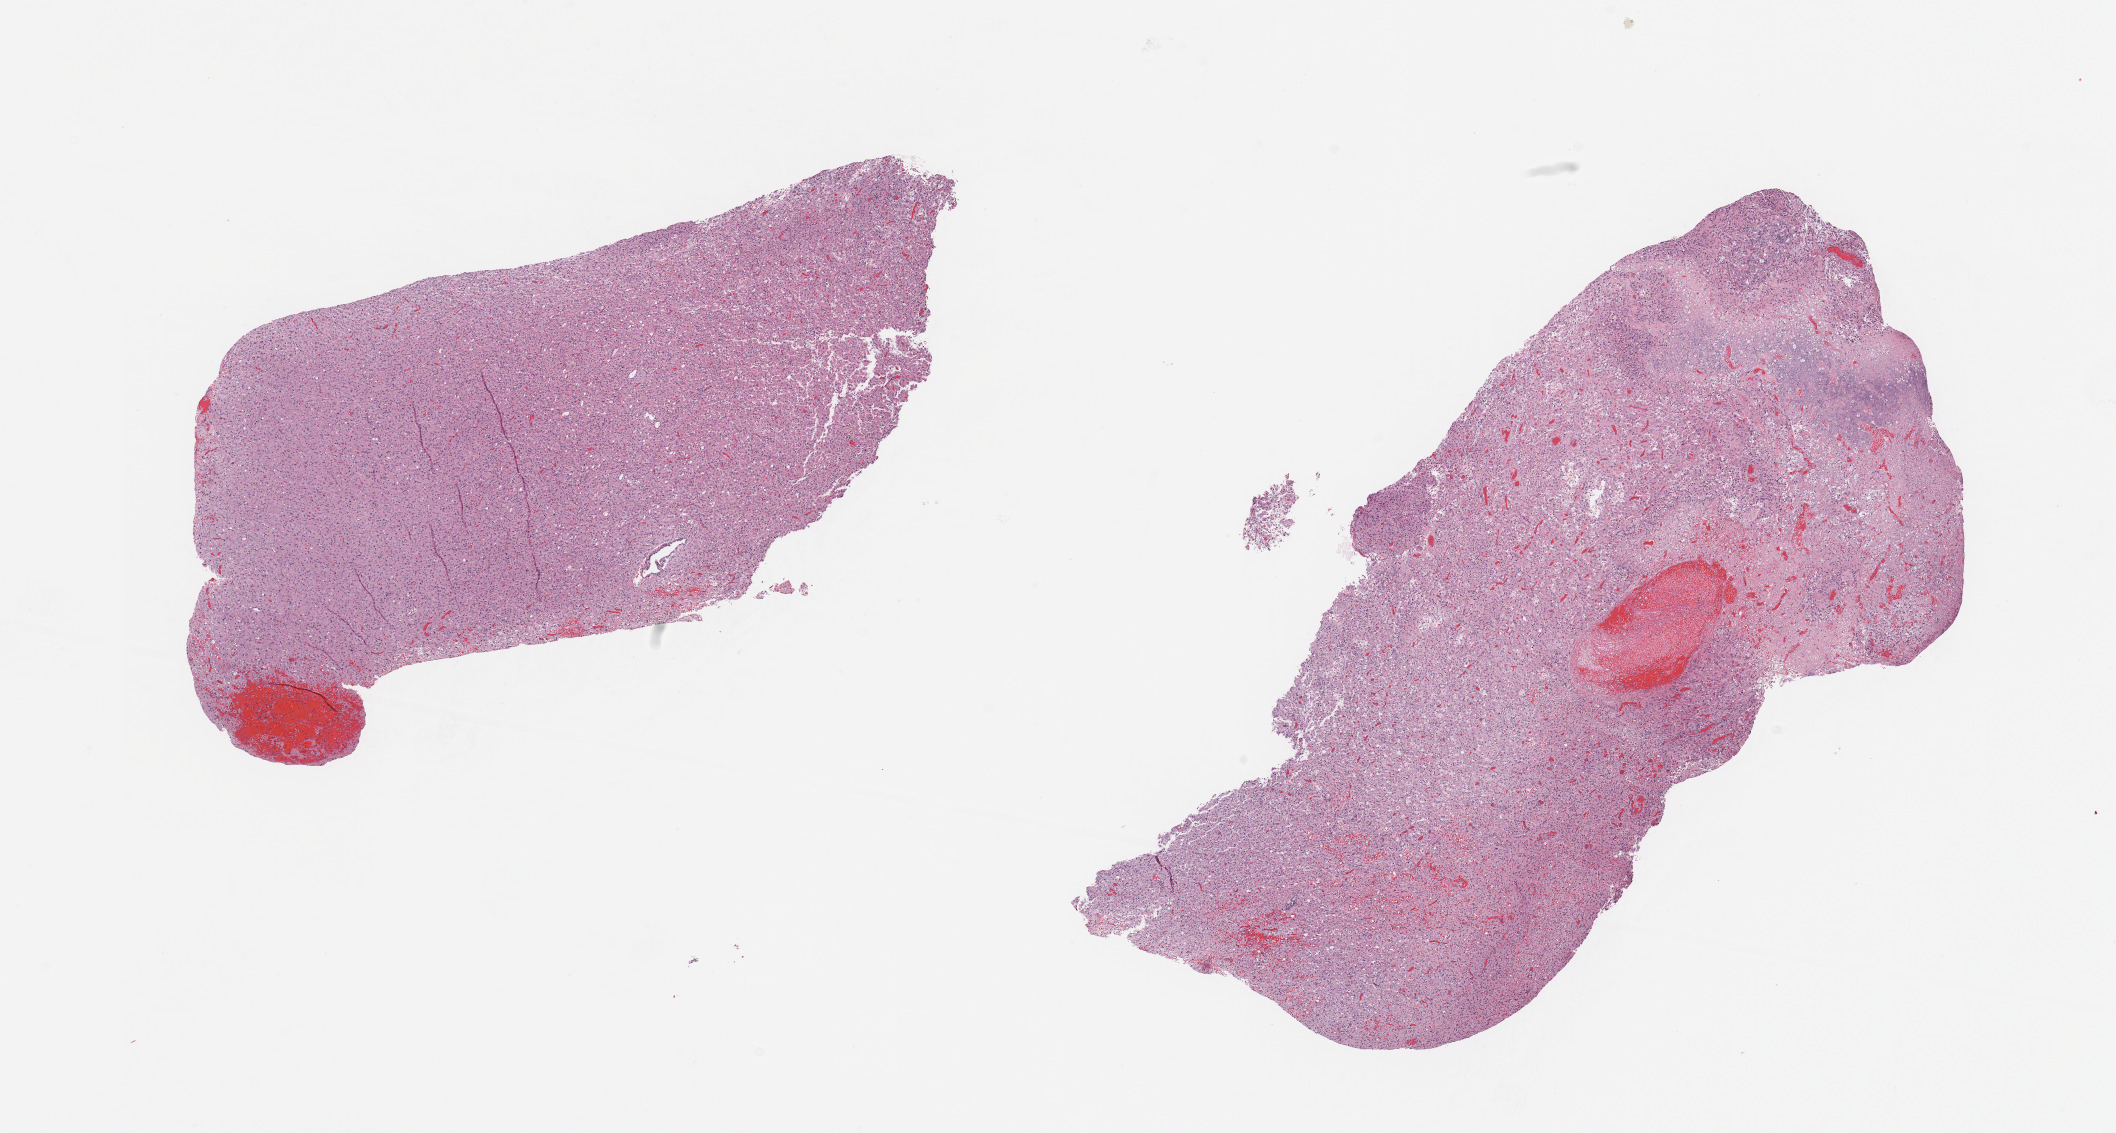
Hematoxylin and eosin (H&E) stained whole-slide image — a low-resolution overview of the entire scanned area, about 16.7 x 9.0 mm (slide scanned at 20x). Tumour tissue sample, sampled site: brain. Patient: female, age 62 years. Slide review estimates, as recorded: tumour nuclei 80%, necrosis 10%.
Primary tumour site (as recorded): temporal lobe. Histologic diagnosis: Glioblastoma.